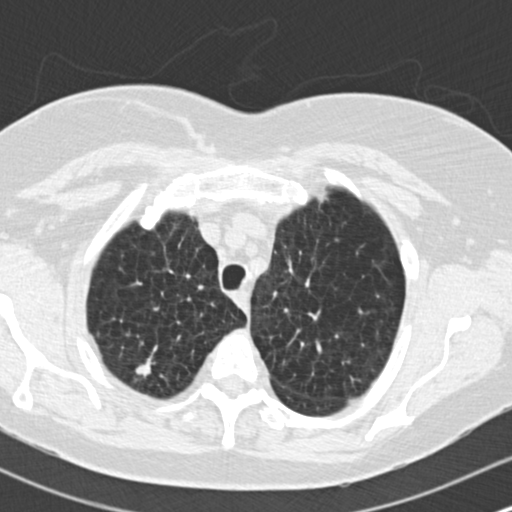
Low-dose screening chest CT, axial slice. Baseline screening round. Lung window (W 1500 / L -600 HU). Female participant, aged 73 years at enrolment. Former smoker at enrolment.
Expert reader's lesion annotation, bounding box [x1, y1, x2, y2] px = [120, 336, 174, 388]. The screening reader recorded 2 non-calcified nodules or masses ≥4 mm on this exam; which of them this box marks is not recorded. Official screen result: positive, change unspecified: nodule(s) >= 4 mm or enlarging nodule(s), mass(es), or other non-specific abnormalities suspicious for lung cancer. Later outcome: lung cancer diagnosed 601 days after this screen — adenocarcinoma, NOS, right upper lobe, moderately differentiated (G2), stage IB (AJCC 6th edition), 15 mm at pathology.